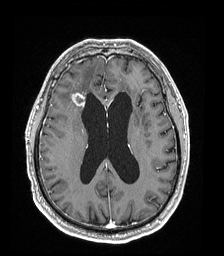
Brain MRI from a brain-tumour surgery series, one axial slice; position 79 of 192 along the scan axis; T1-weighted post-contrast; 224 × 256 image matrix, field of view 224 × 256 mm. From the clinical record (not read from this slice): histopathology: Astrocytoma; WHO grade: 4; IDH mutation: yes.
Outlined on this slice (manually delineated by an expert):
- tumour: bounding box <70,93,85,108> (left, top, right, bottom; pixels)